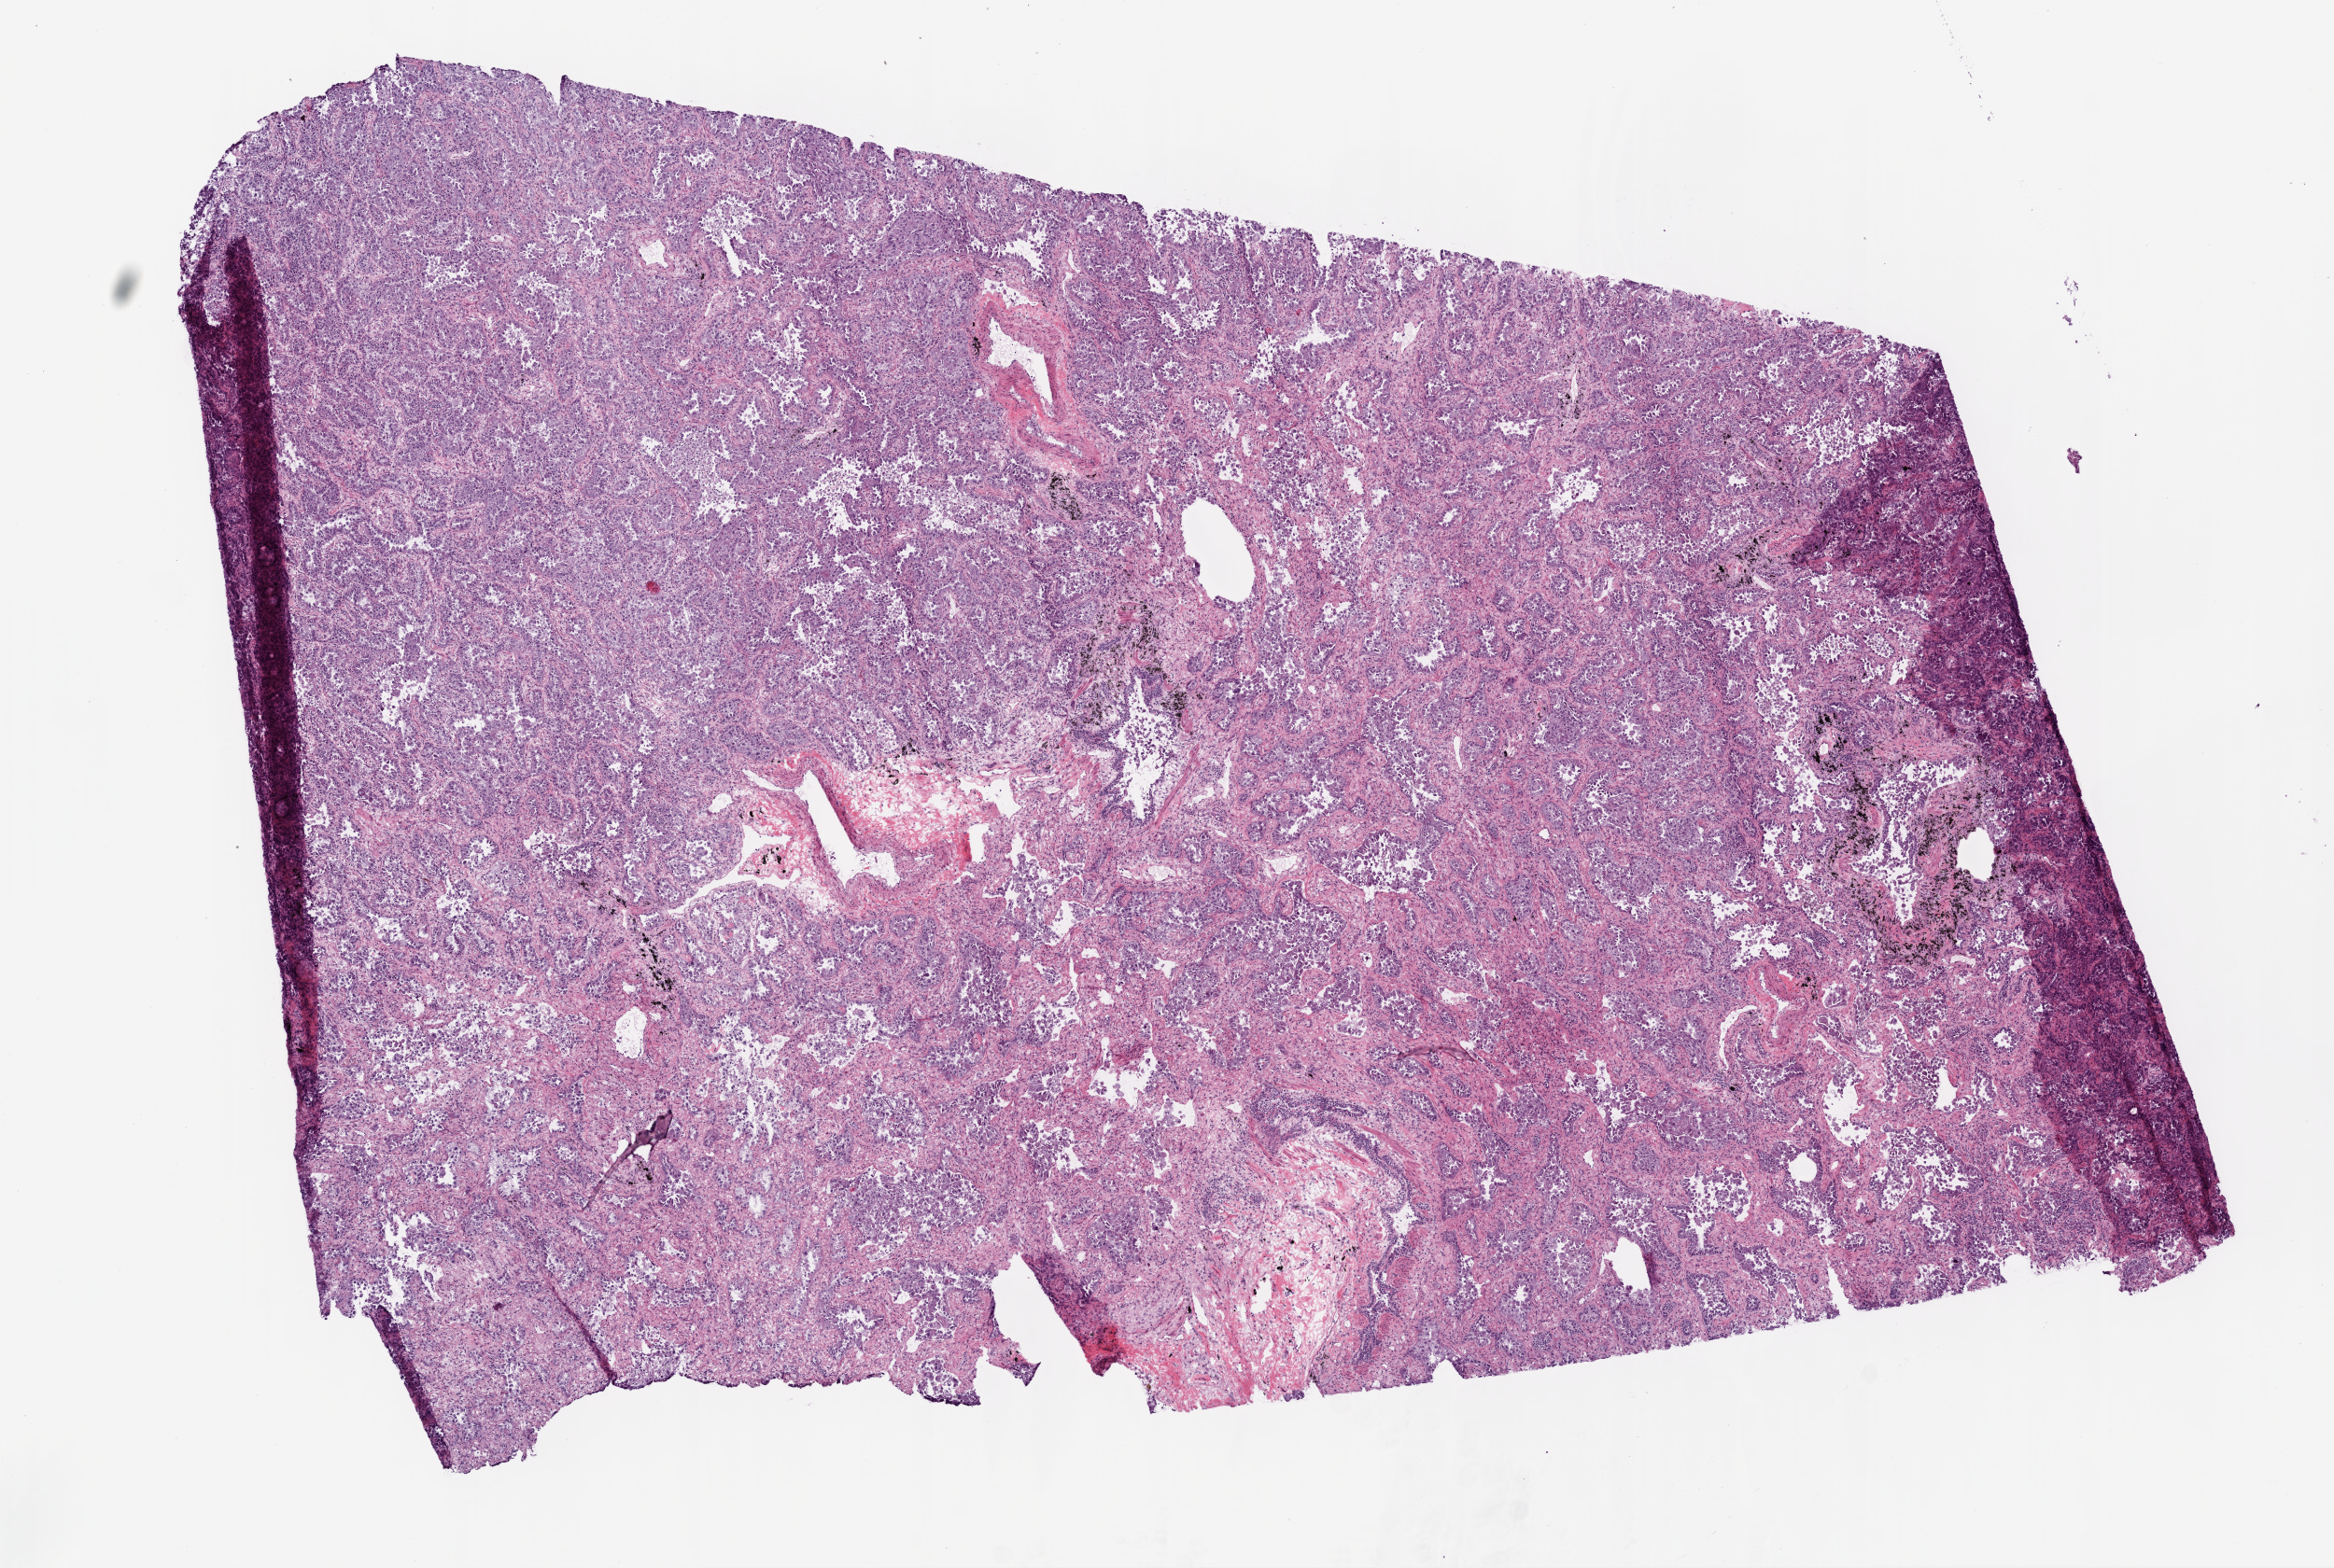
Digitized Hematoxylin and eosin (H&E) stained tissue section (whole slide) — whole scanned area (about 10.0 x 6.7 mm, from a 20x scan) shown as a low-resolution overview, frozen section, sample: primary tumour, lung. Female, age 70 years at initial diagnosis. Pathologist review of this section (percent, as recorded): tumour cells 82%, tumour nuclei 80%, normal cells 5%, stromal cells 10%, necrosis 3%.
• TNM: T1 N0 M0
• laterality: right
• AJCC pathologic stage: IA
• histologic diagnosis: Adenocarcinoma, NOS (upper lobe, lung)